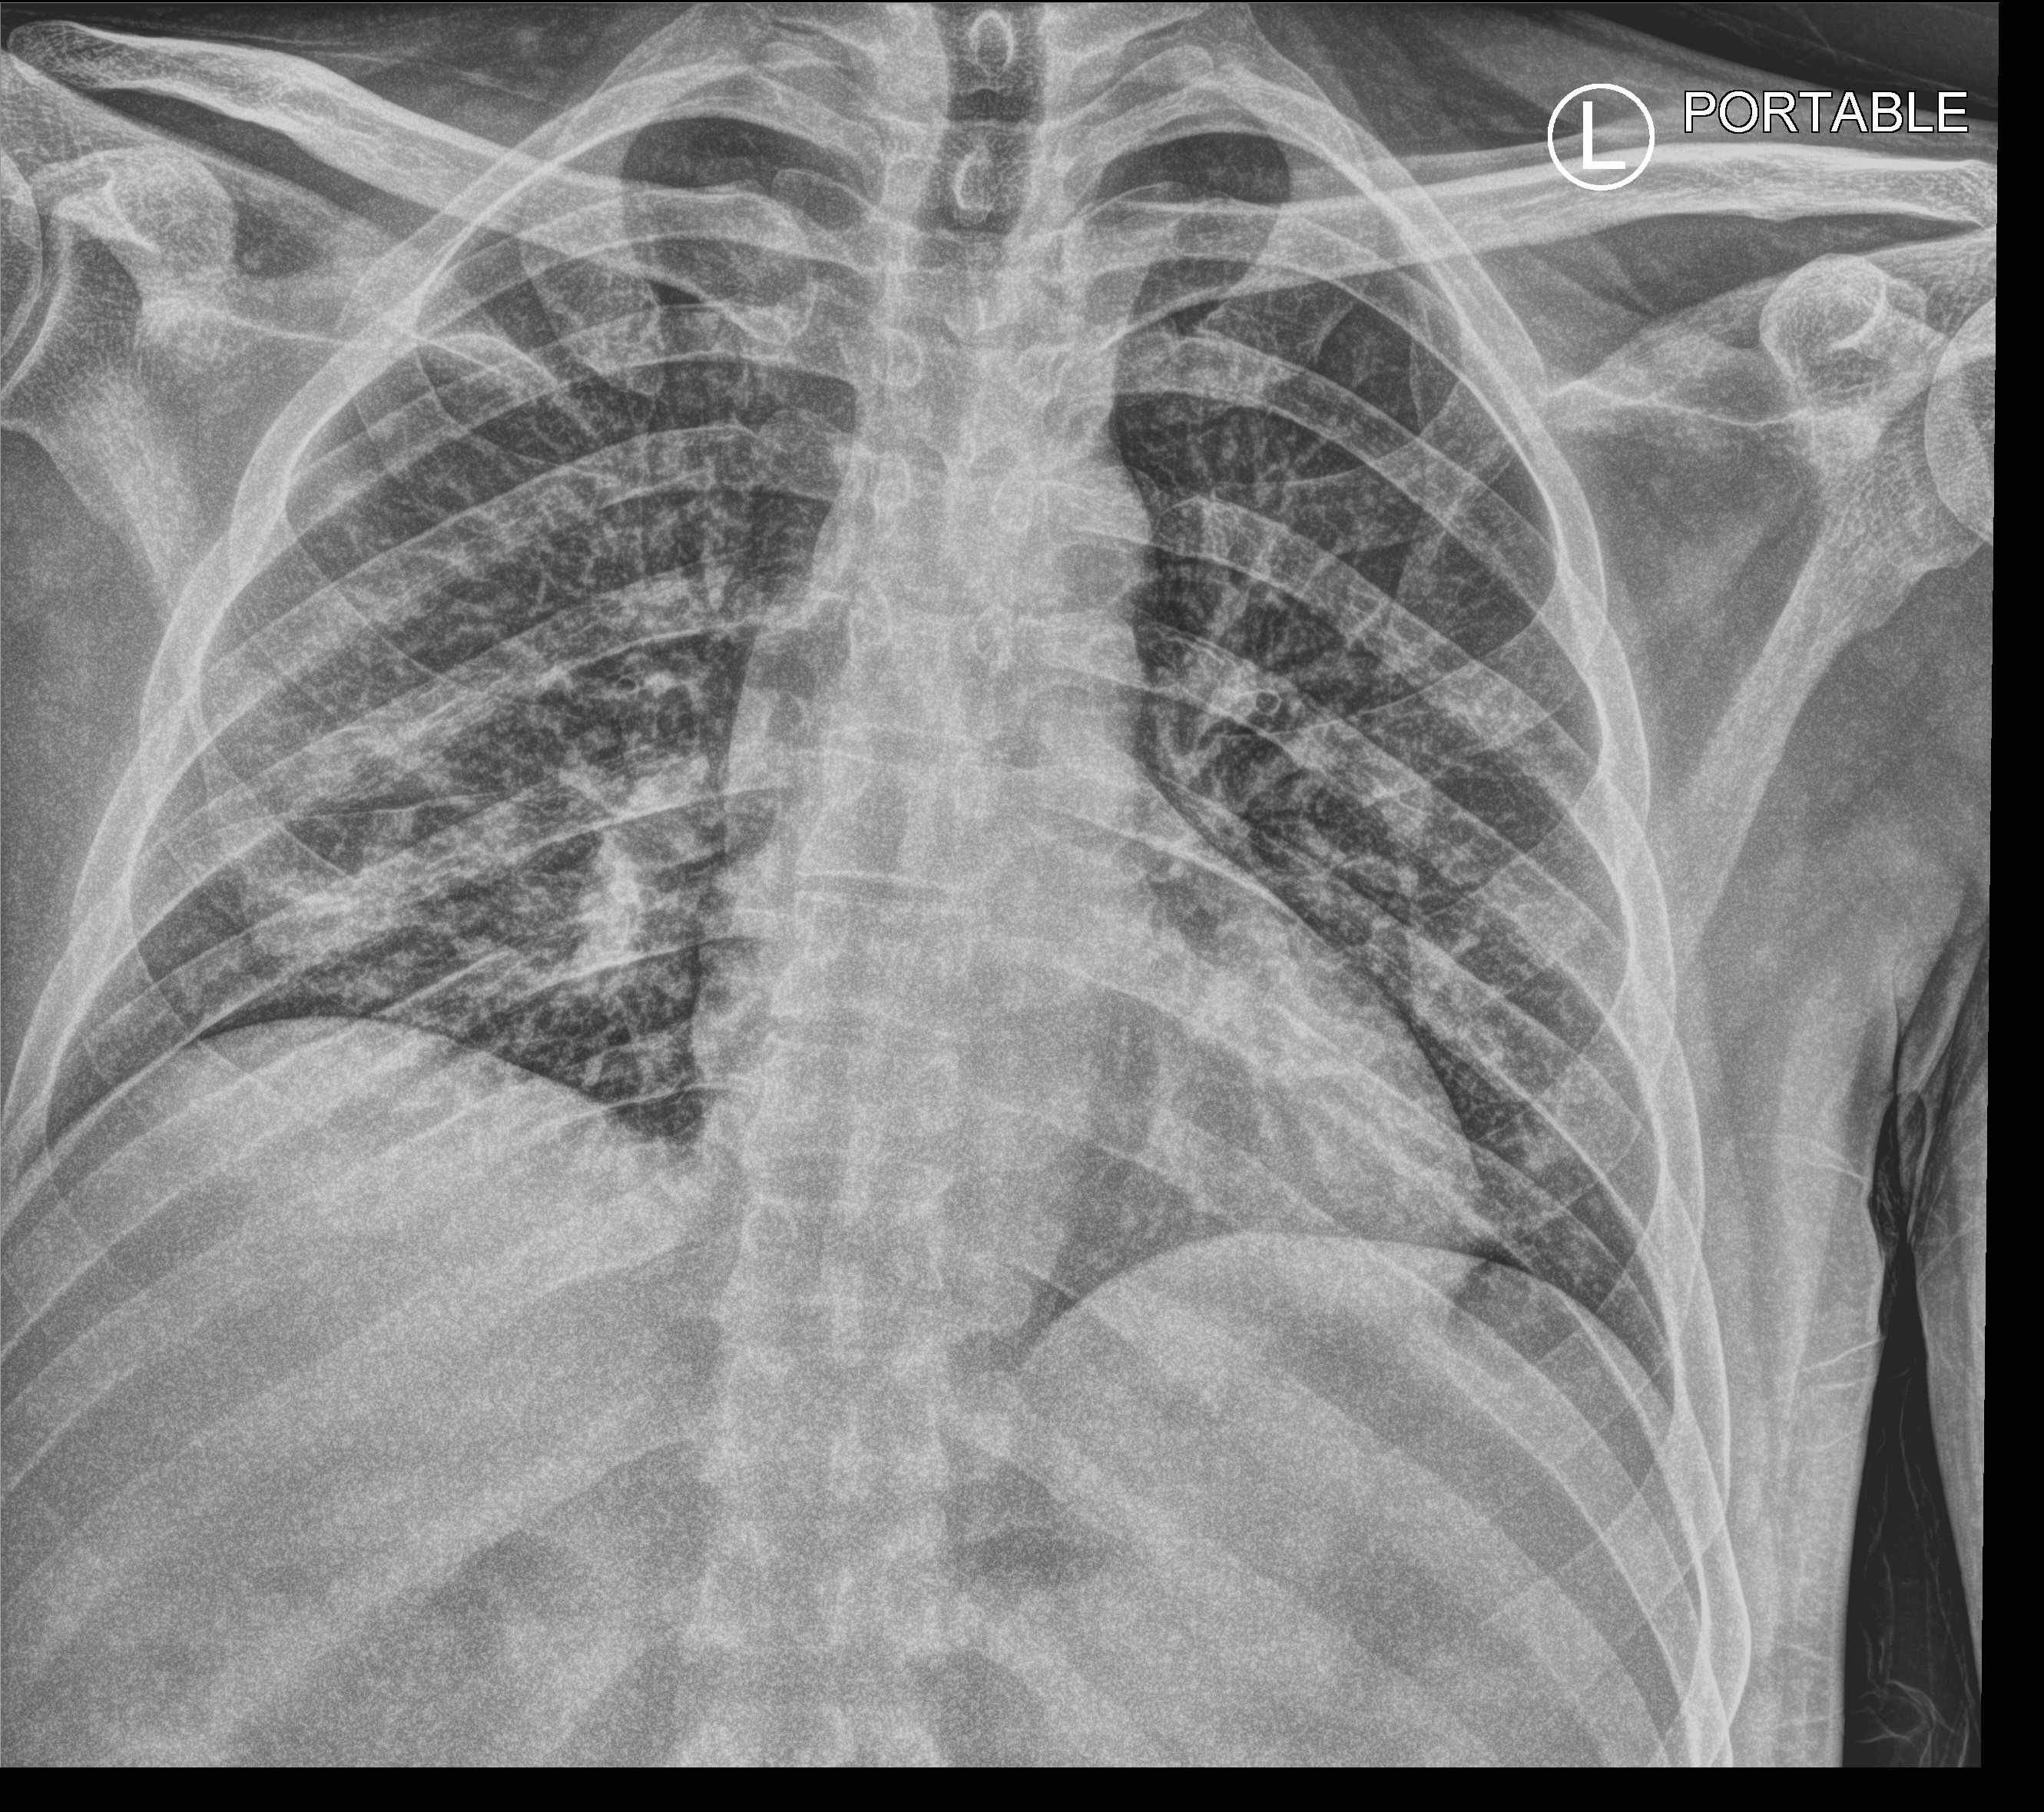
Chest X-ray (portable). Patient hospitalised with COVID-19; male, aged 18–59 years.
From the hospital-stay record, not from the radiograph (when in the stay this image was taken is not recorded): mechanically ventilated during this hospital stay: no; length of hospital stay: 3 days; chronic kidney disease (admission record): no.